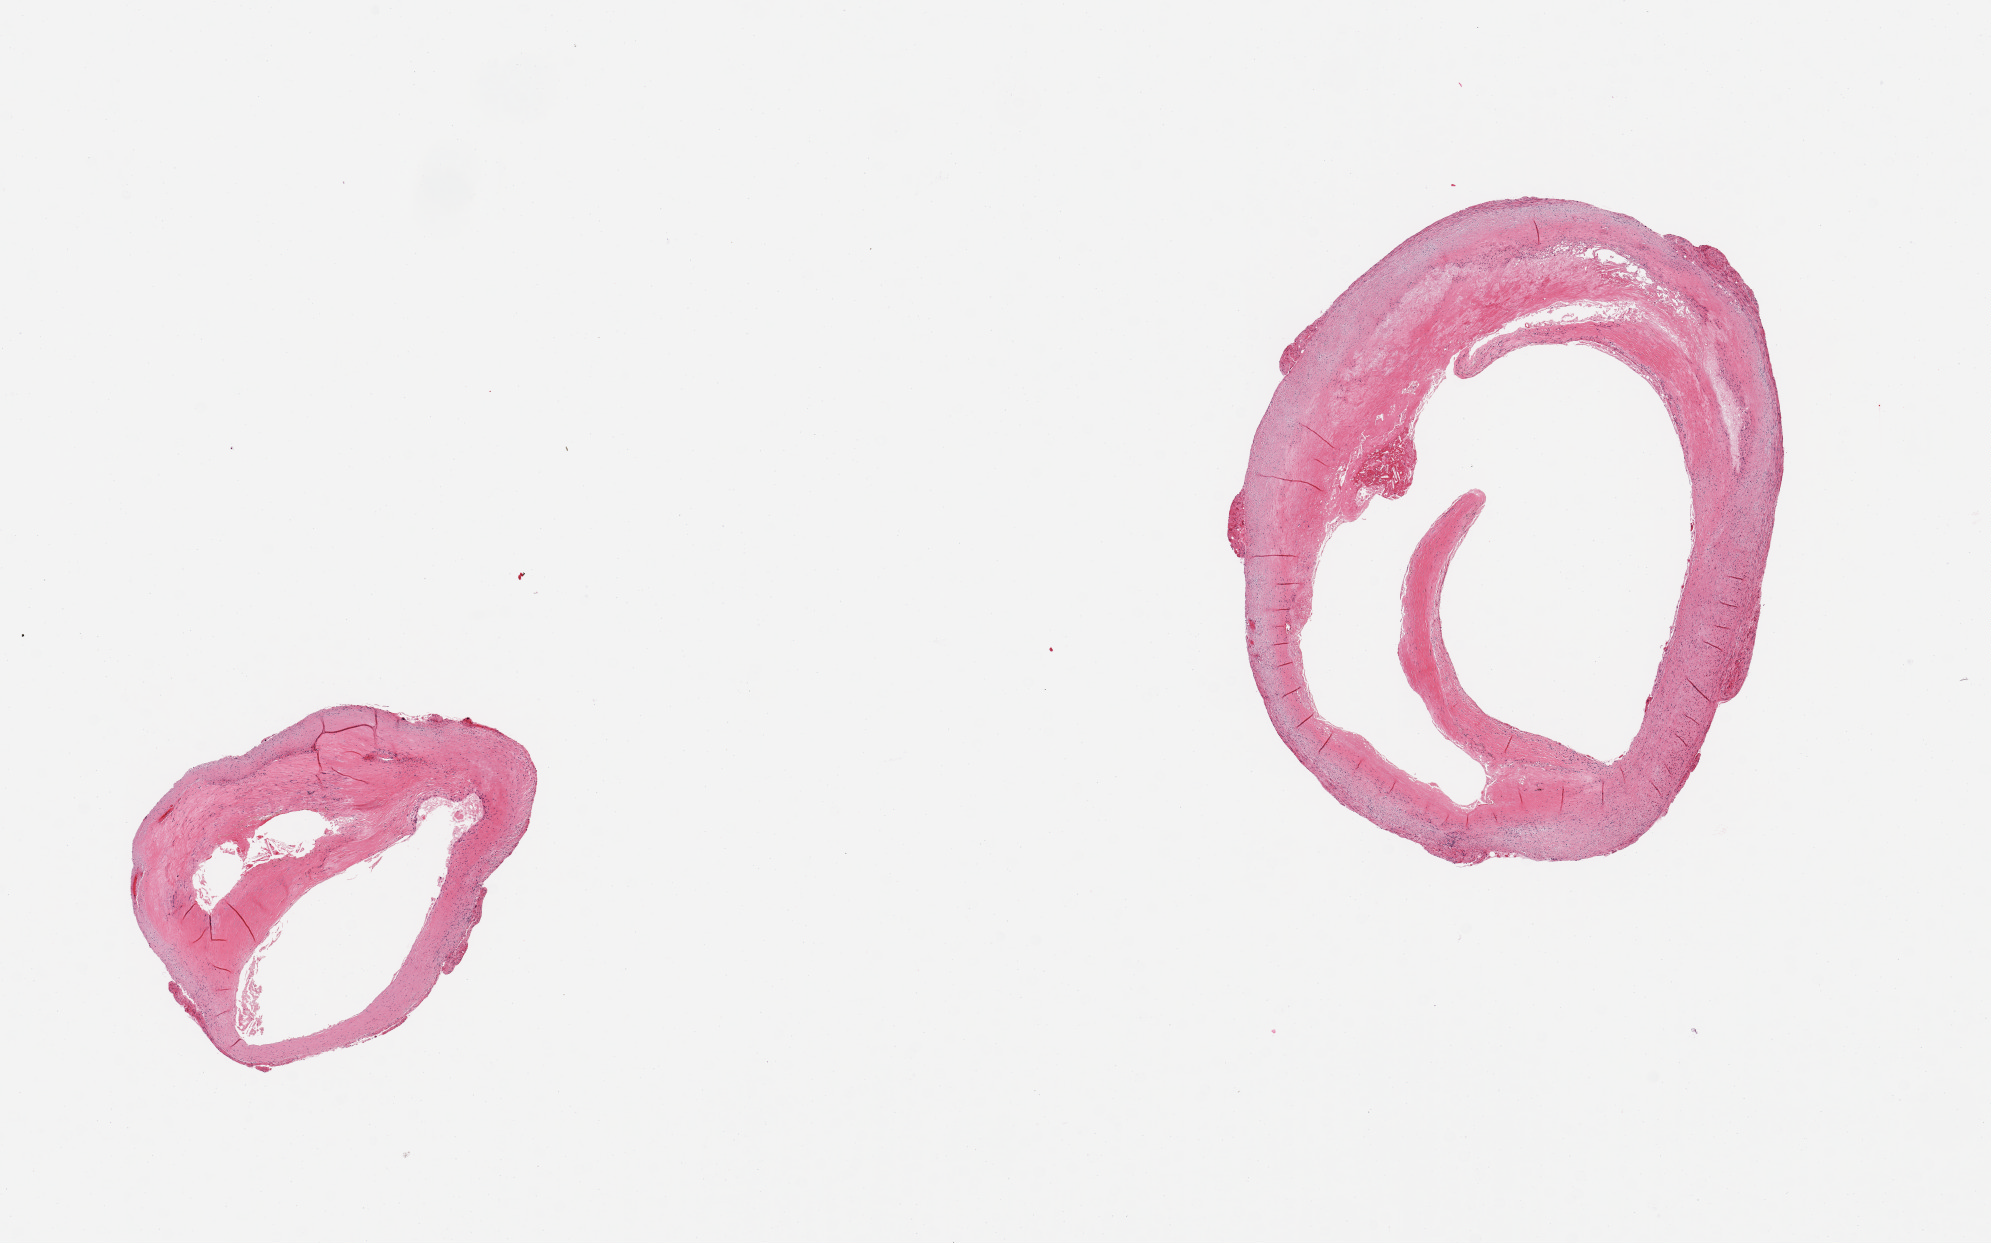
H&E whole-slide image, brightfield — shown as a low-resolution overview of the whole scanned area (about 15.8 x 9.8 mm), PAXgene-fixed, paraffin-embedded tissue, section of coronary artery (target tissue), donor tissue sample. Donor sex: male.
Pathologist's review note for this sample: 2 pieces, ~60% occlusvie atherosis.